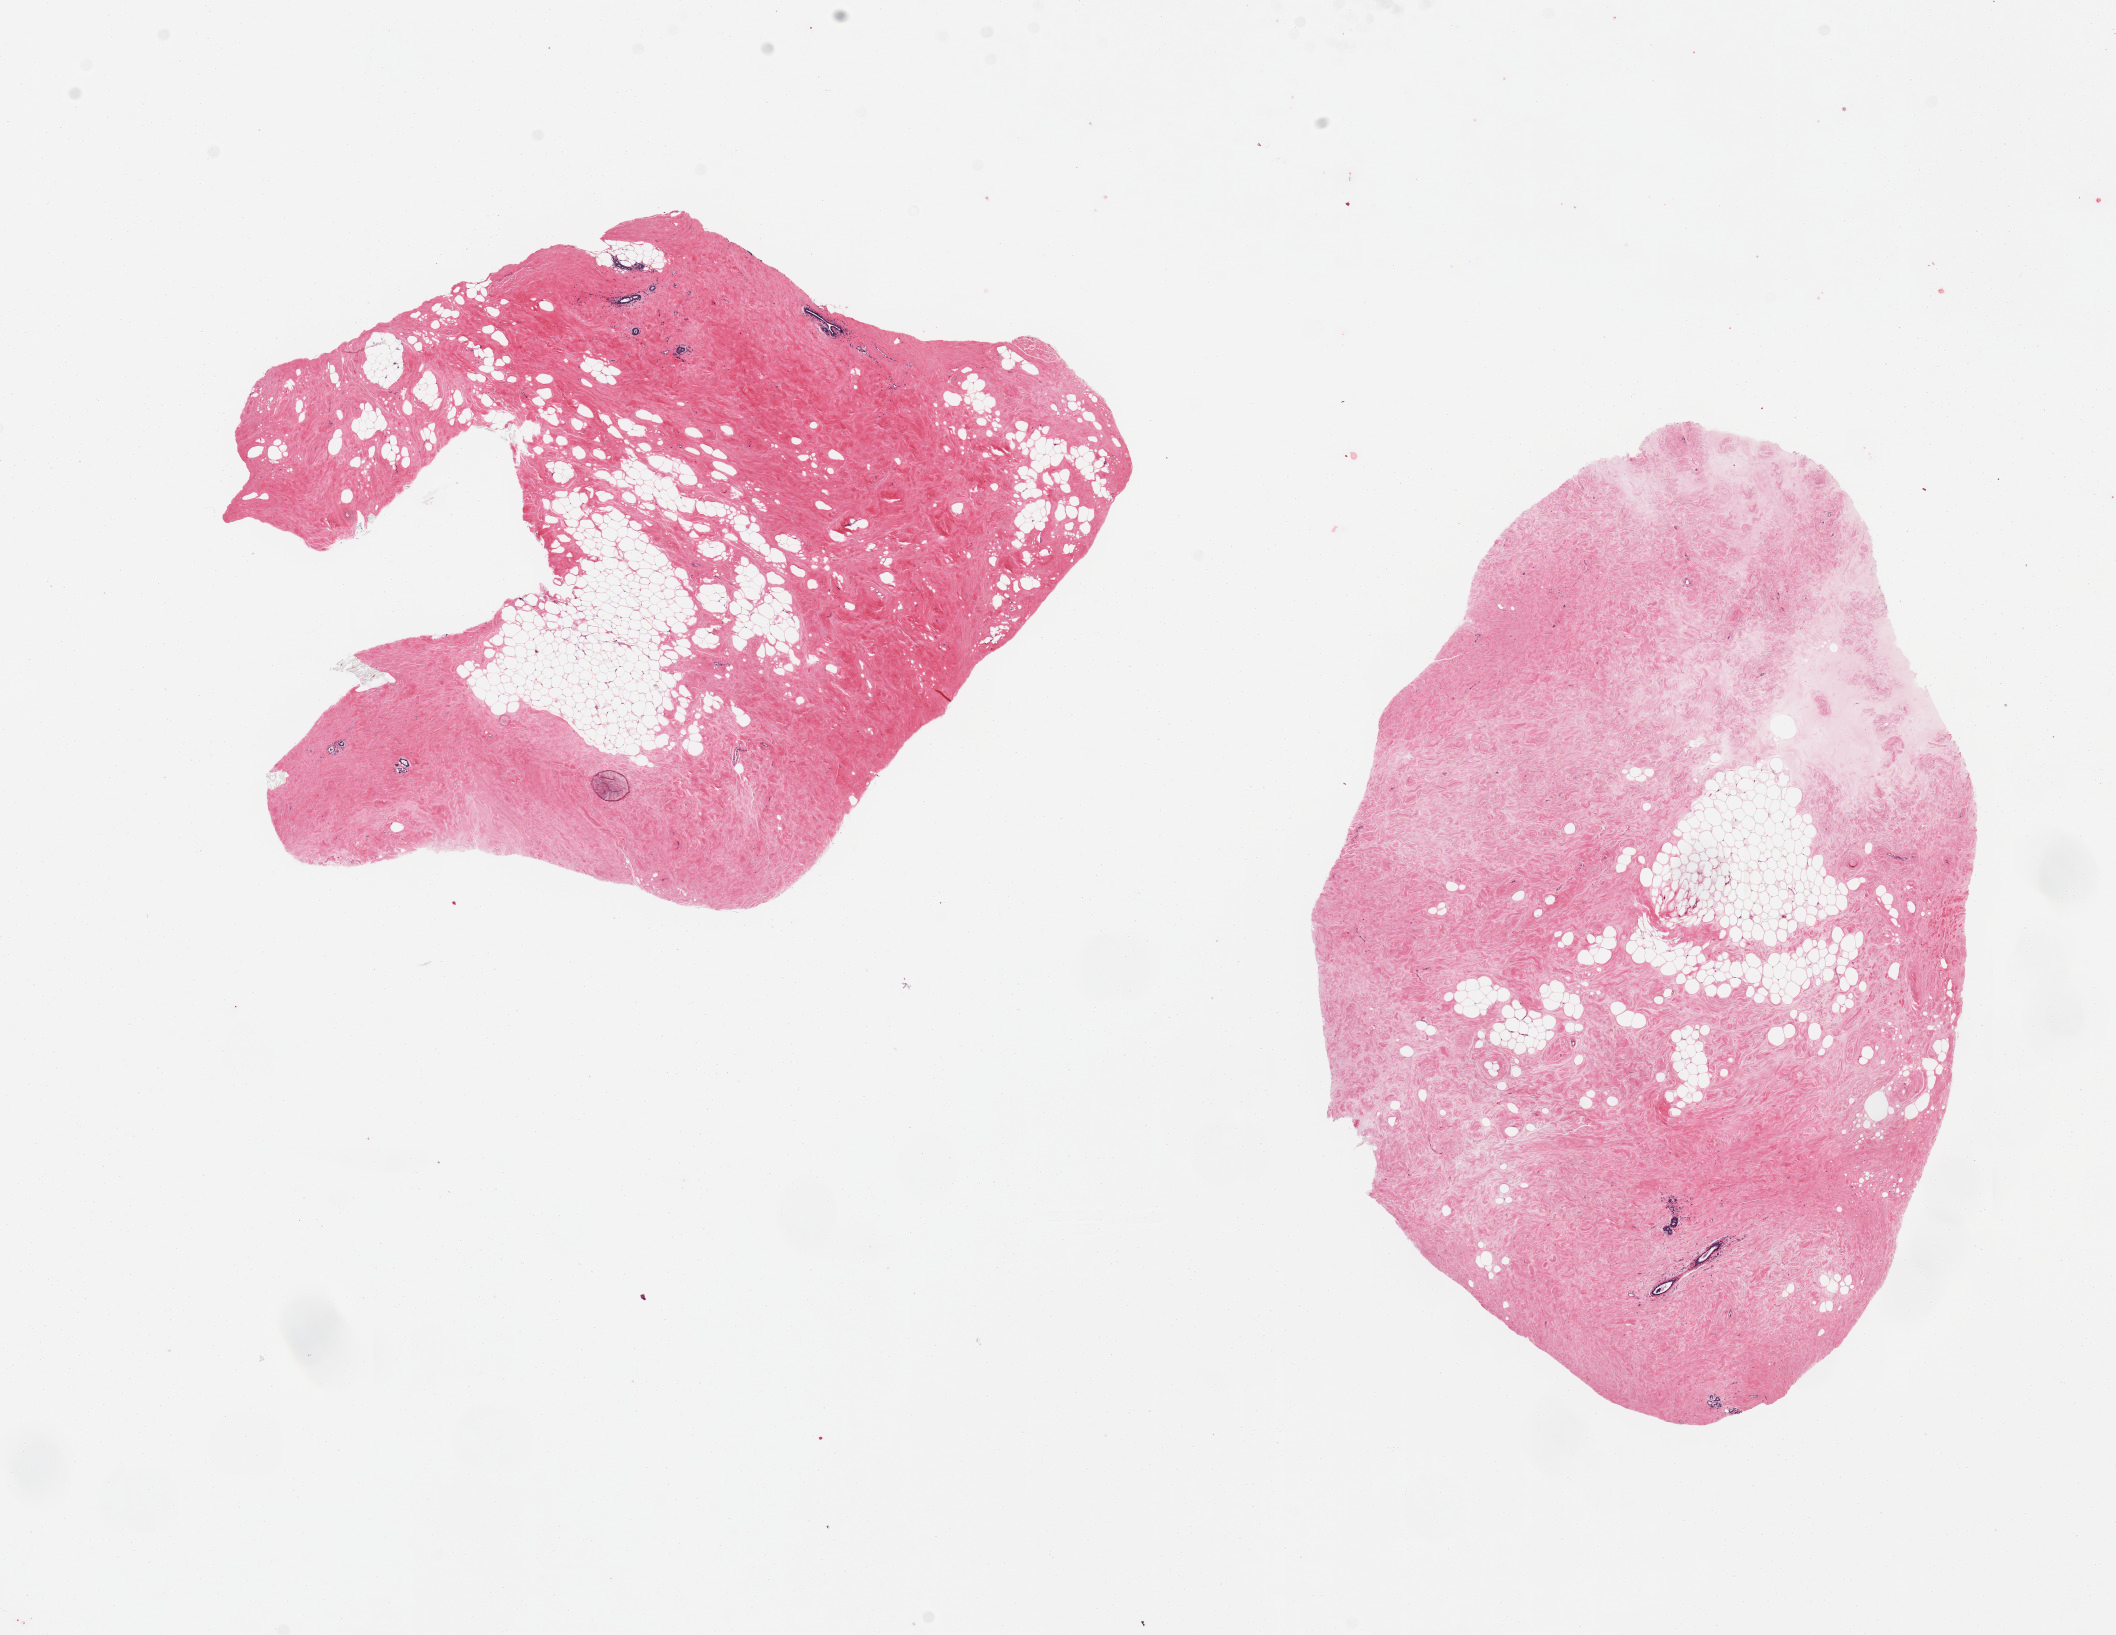
Whole-slide image, H&E stain, brightfield — a low-resolution overview of the entire scanned area, about 16.7 x 12.9 mm; PAXgene-fixed paraffin-embedded (PFPE) section; target tissue: breast; tissue donor sample.
* reviewer comment on this tissue sample: 2 pieces; rare ductal structures embedded in fibroadipose stroma